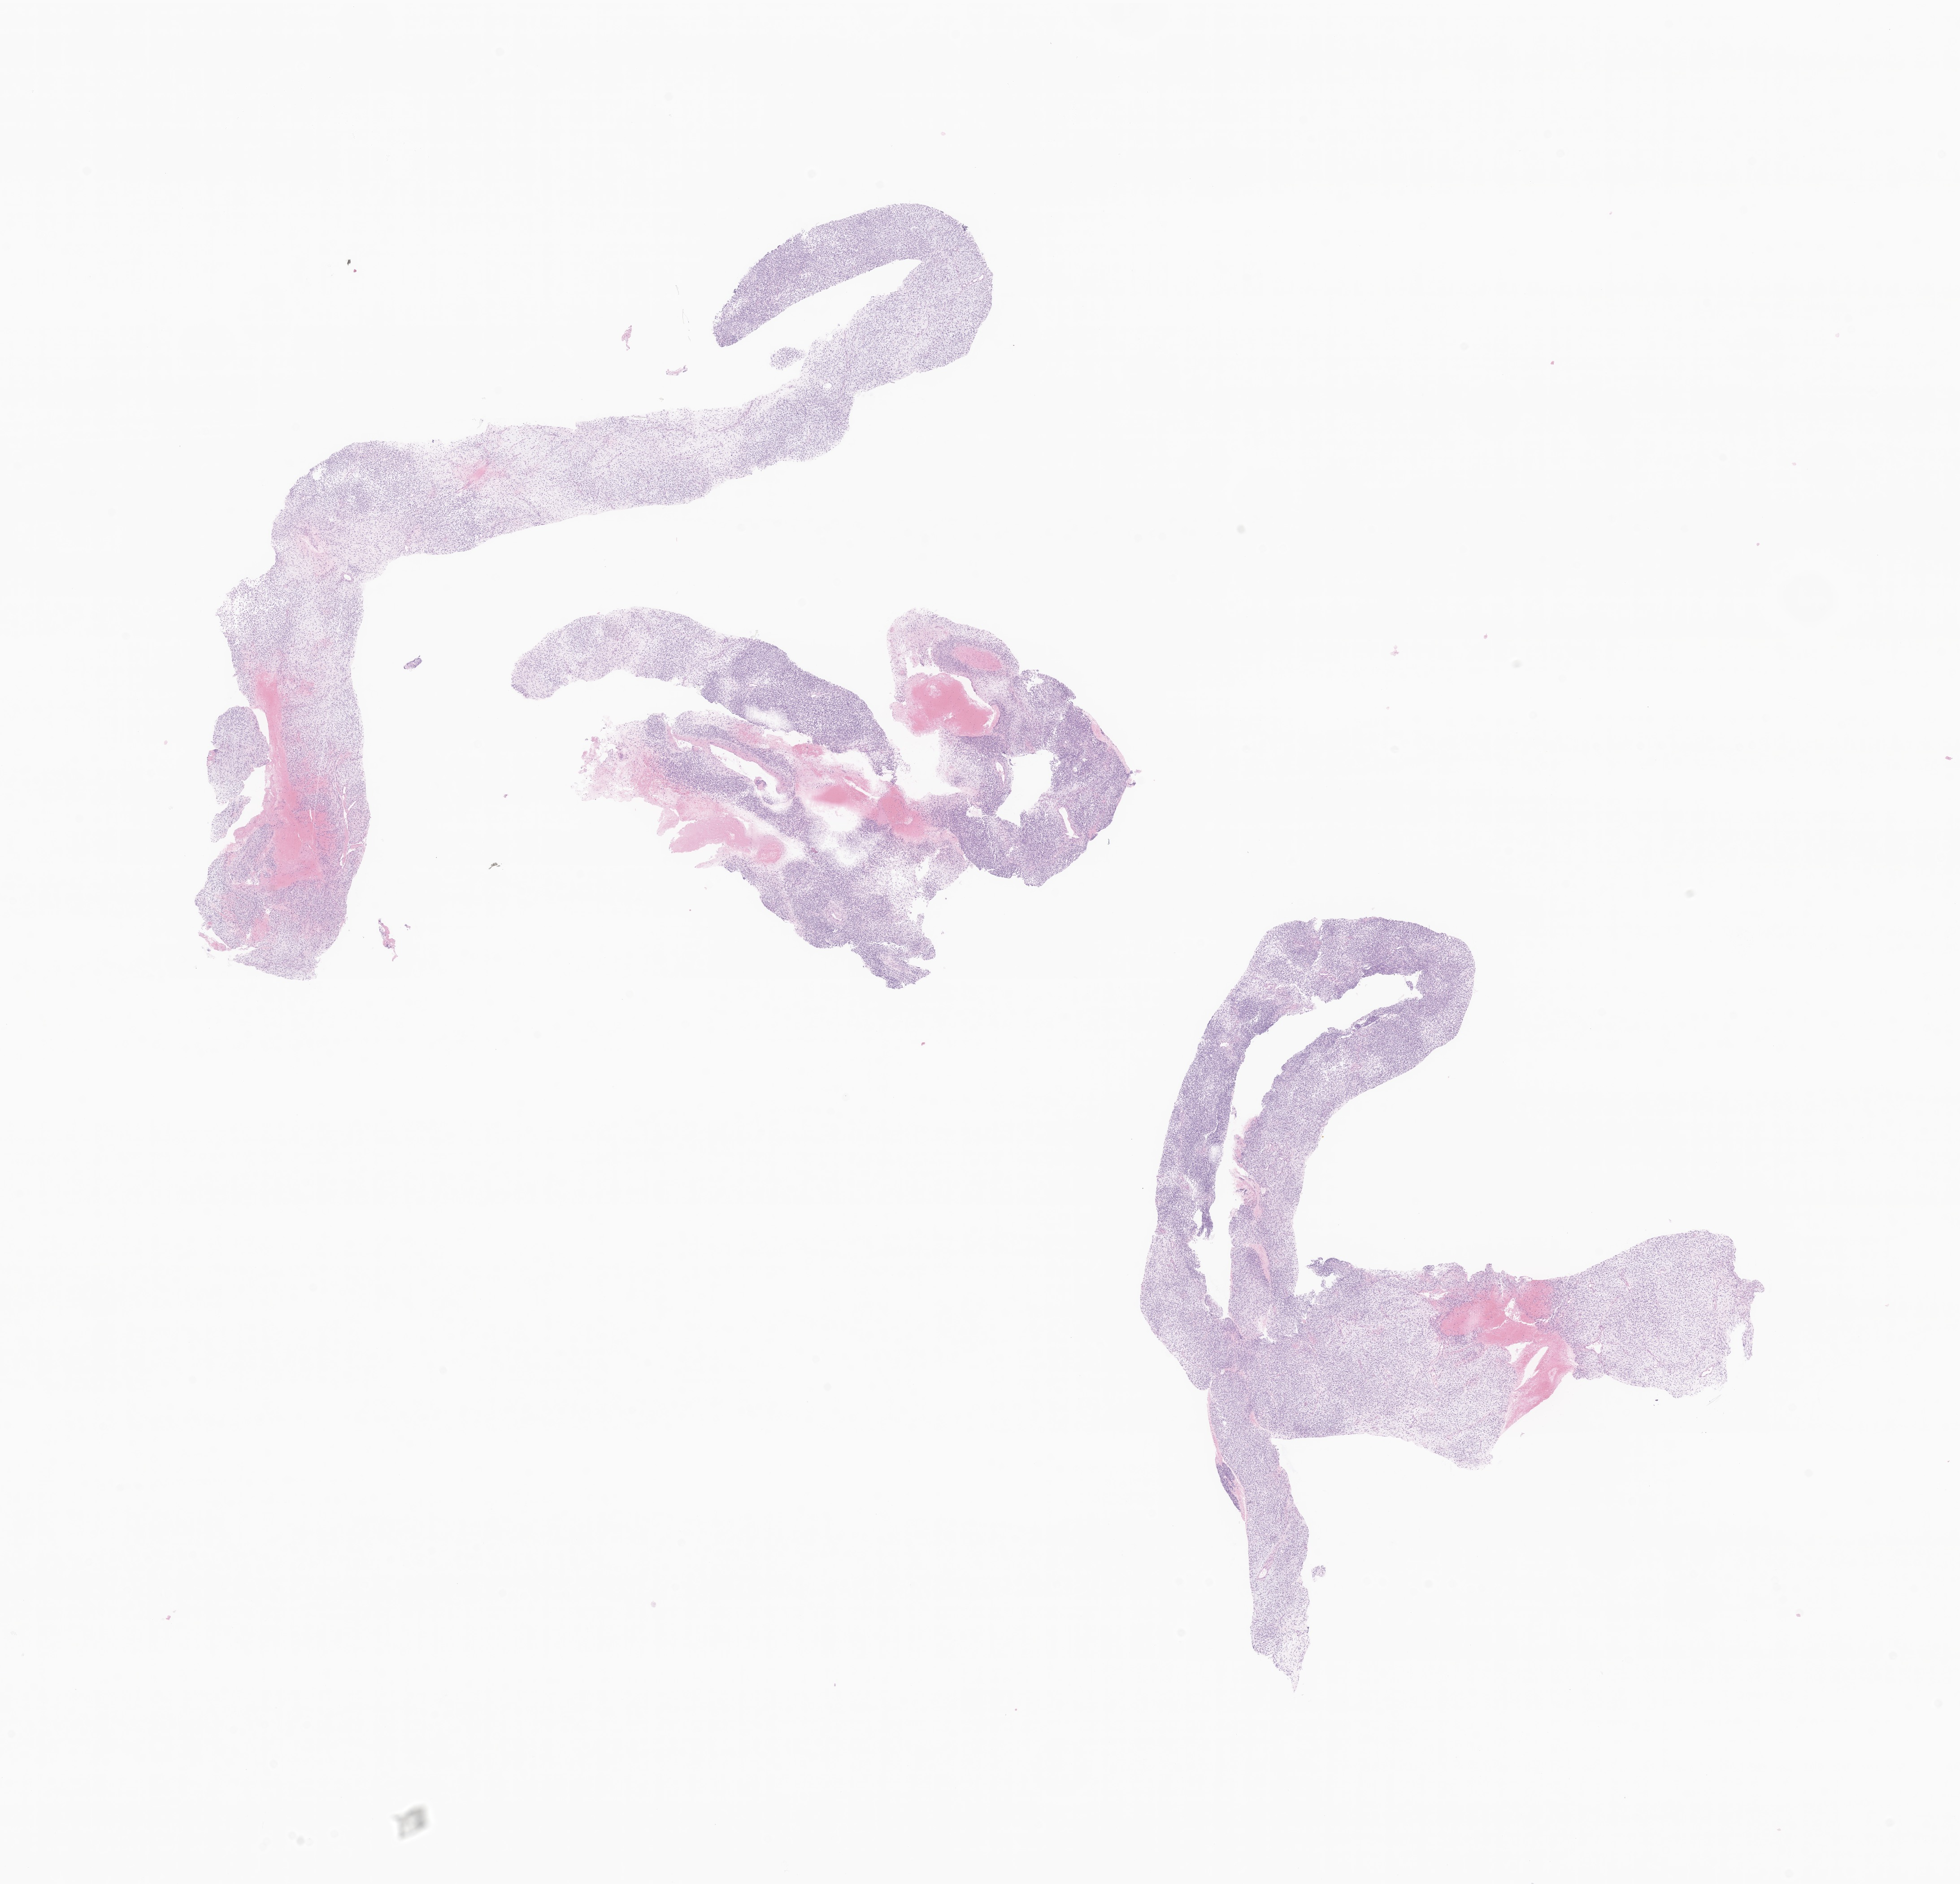
Whole-slide image, hematoxylin and eosin (H&E) stain of tumor tissue from the abdomen, shown as a low-resolution overview of the whole scanned area (about 18.4 x 17.7 mm), formalin-fixed paraffin-embedded section. Patient male; age 584 days (about 1.6 years).
Diagnosis (ICD-O-3 morphology term): Embryonal rhabdomyosarcoma, NOS.